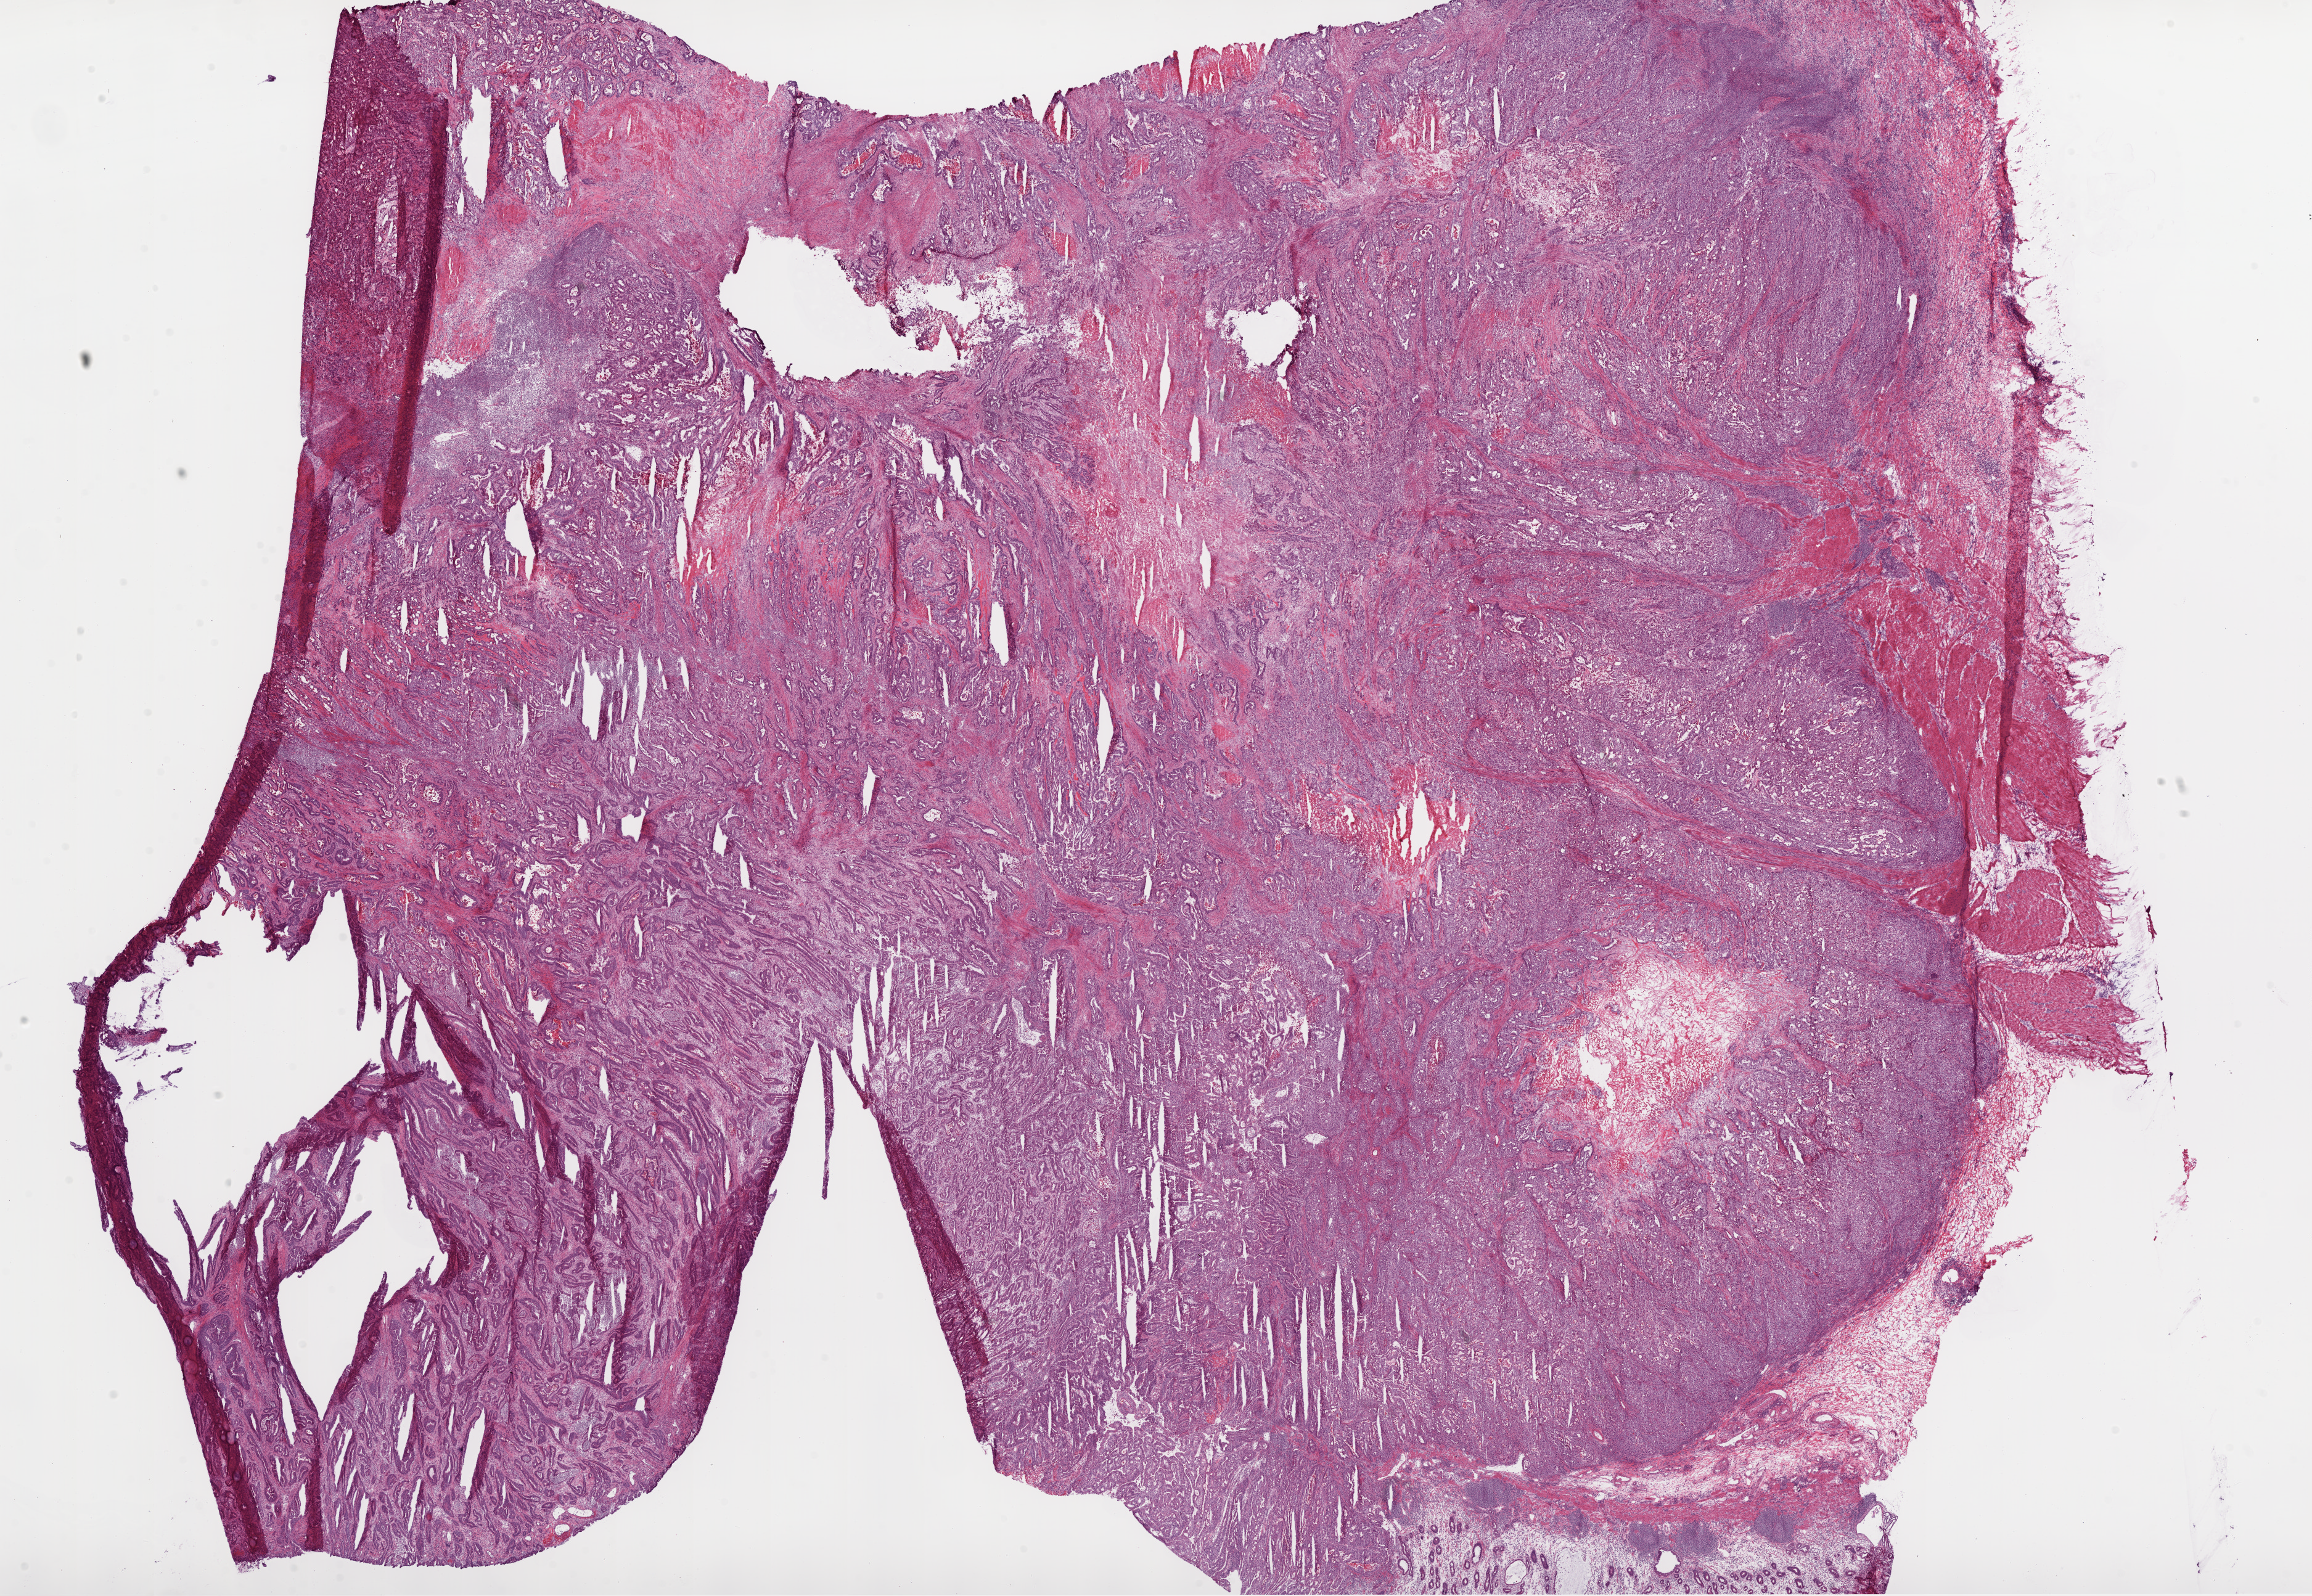
Digitized Hematoxylin and eosin (H&E) stained tissue section (whole slide) — low-resolution overview of the scanned area, about 30.1 x 20.8 mm (acquisition: 20x scan), frozen section, sample: primary tumour, stomach. Patient: male, age at initial diagnosis 70 years. Histologic grade: G2 (moderately differentiated). Pathologist review of this section (percent, as recorded): tumour cells 85%, tumour nuclei 85%, normal cells 2%, stromal cells 10%, necrosis 3%.
* AJCC pathologic stage: IIIA (6th edition)
* pathologic diagnosis: Adenocarcinoma, NOS (gastric antrum)